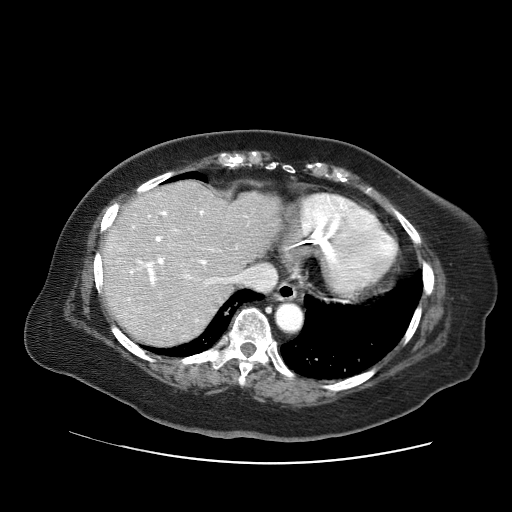
Contrast-enhanced abdominal CT (liver protocol), one axial slice. Position 52 of 71 along the scan axis. 120 kVp. Soft-tissue window (W 400 / L 40 HU). 2.5 mm slice thickness. 512 × 512 image matrix, field of view 400 × 400 mm. Case-level facts recorded for this patient, not image findings: diagnosis: hepatocellular carcinoma (patient treated with transarterial chemoembolisation; whether this scan precedes or follows treatment is not stated here); TNM stage (as recorded): Stage-II; Child-Pugh class: A; tumour differentiation: poorly differentiated; tumour nodularity: multinodular.
Outlined on this slice (semi-automatically segmented with operator editing):
- liver parenchyma outside the tumour (the mass and vessels are separate outlines, so this box may not span the whole liver): bounding box [x1, y1, x2, y2] px = [102, 180, 281, 344]
- liver vessels: [110, 210, 232, 322]